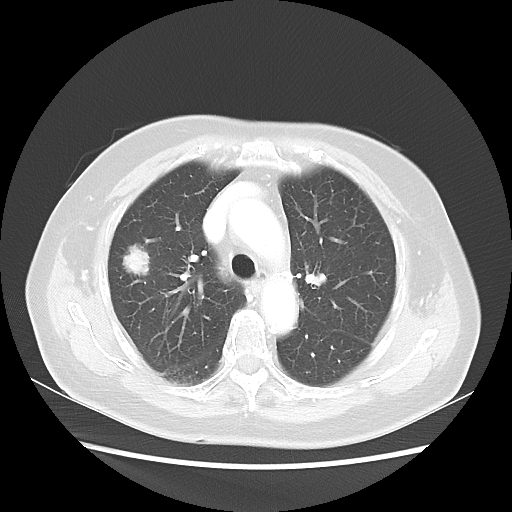
Chest CT, one axial slice. Position 33 of 48 along the scan axis. Reconstruction kernel LUNG. Lung window (W 1500 / L -600 HU). 5 mm slice thickness. 512 × 512 image matrix, field of view 360 × 360 mm. Female patient, age 75 years. Case-level facts recorded for this patient, not image findings: clinical TNM (as recorded): T1c N0 M0.
Outlined on this slice (bounding box drawn by a radiologist):
- lung tumour (recorded histology: adenocarcinoma): bounding box <118,240,152,284> (left, top, right, bottom; pixels)